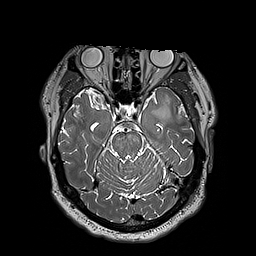
Brain MRI from a brain-tumour surgery series, one axial slice; 1 mm slice thickness; 256 × 256 image matrix, field of view 250 × 250 mm. From the clinical record (not read from this slice): histopathology: Astrocytoma; WHO grade: 3; IDH mutation: yes; tumour location: Left Insular.
Outlined on this slice (expert manual segmentation):
- tumour: bounding box <152,97,170,122> (left, top, right, bottom; pixels)